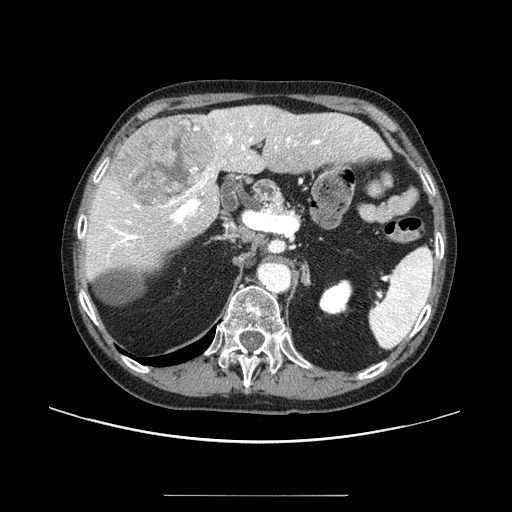
Contrast-enhanced abdominal CT (liver protocol), one axial slice; slice 54 of 91 in the series (ordered by position); reconstruction kernel STANDARD; one of 2 acquisitions stored at this slice position; soft-tissue window (W 400 / L 40 HU); 2.5 mm slice thickness; 512 × 512 image matrix, field of view 400 × 400 mm. From the clinical record (not read from this slice): diagnosis: hepatocellular carcinoma (patient treated with transarterial chemoembolisation; whether this scan precedes or follows treatment is not stated here); TNM stage (as recorded): Stage-I.
Annotated regions visible in this slice (semi-automatically segmented with operator editing):
- liver parenchyma outside the tumour (the mass and vessels are separate outlines, so this box may not span the whole liver): bounding box [x1, y1, x2, y2] px = [84, 106, 383, 279]
- mass: [112, 115, 216, 210]
- liver vessels: [96, 112, 362, 258]